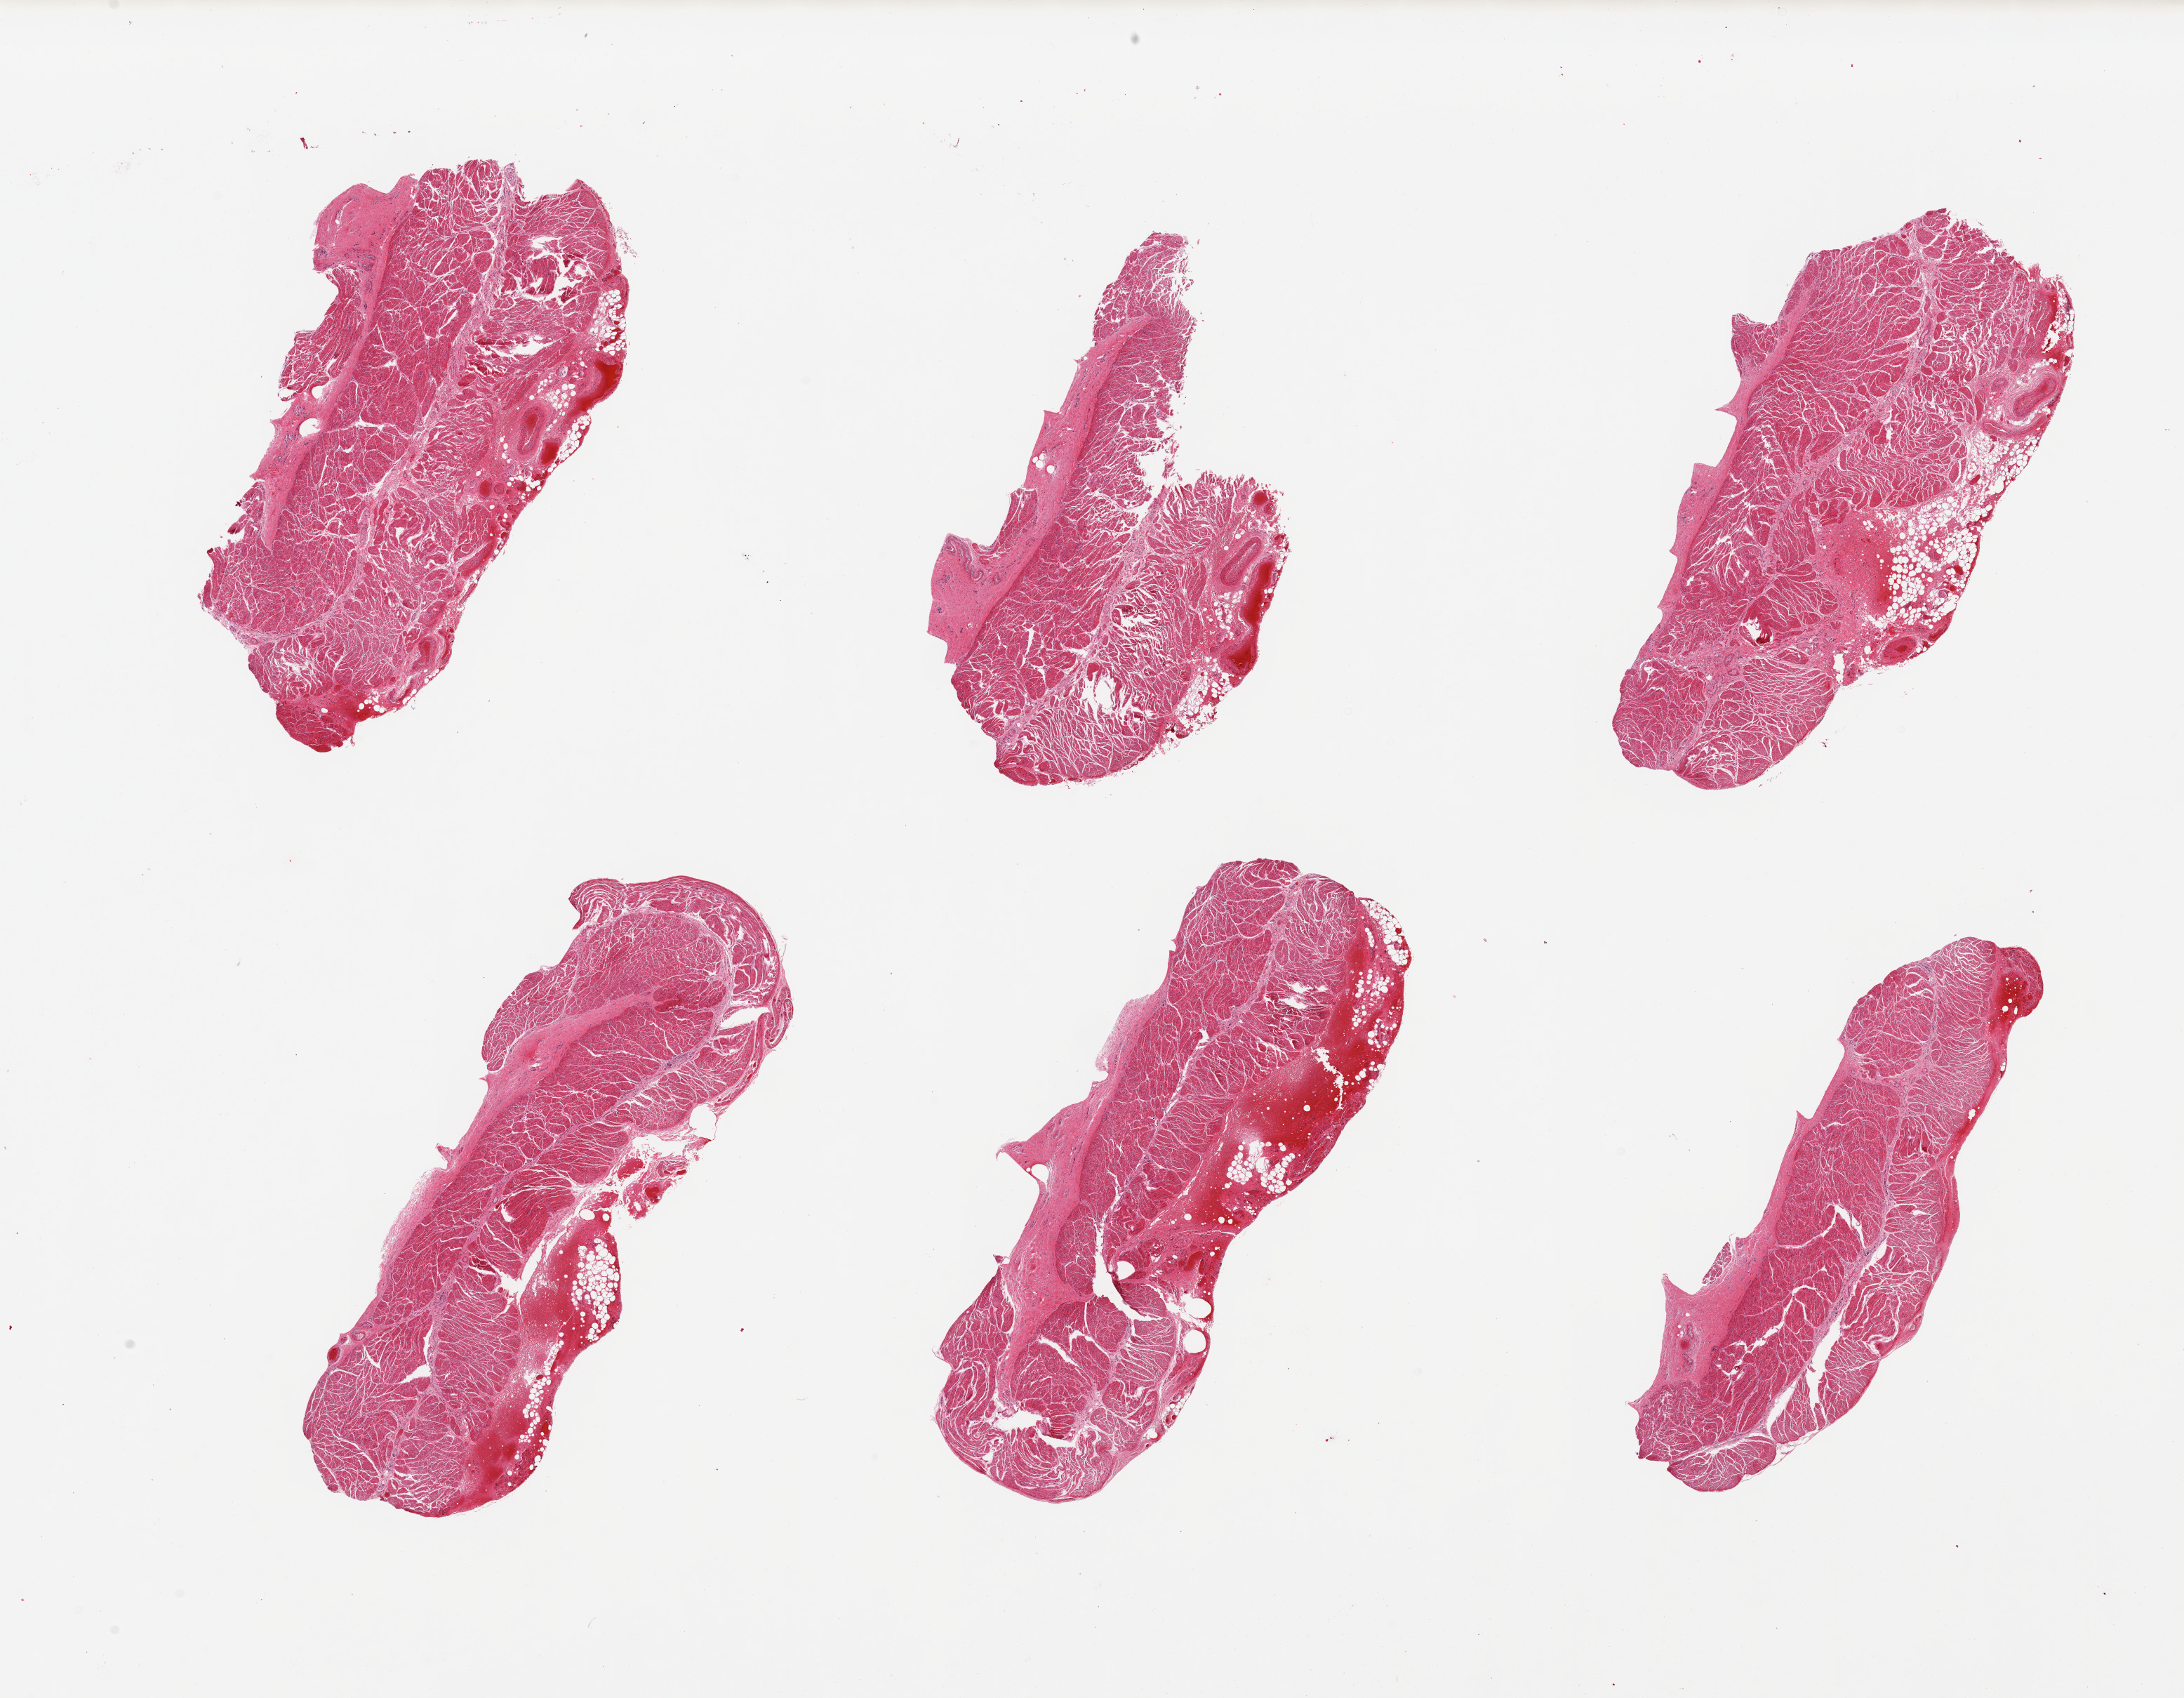
Whole-slide image, H&E stain — shown as a low-resolution overview of the whole scanned area (about 24.6 x 19.1 mm); PAXgene-fixed paraffin-embedded (PFPE) section; sampled site (target tissue): esophageal muscle; tissue donor sample. Donor: female.
Reviewer comment on this tissue sample: 6 pieces, all muscularis, minimal fat.